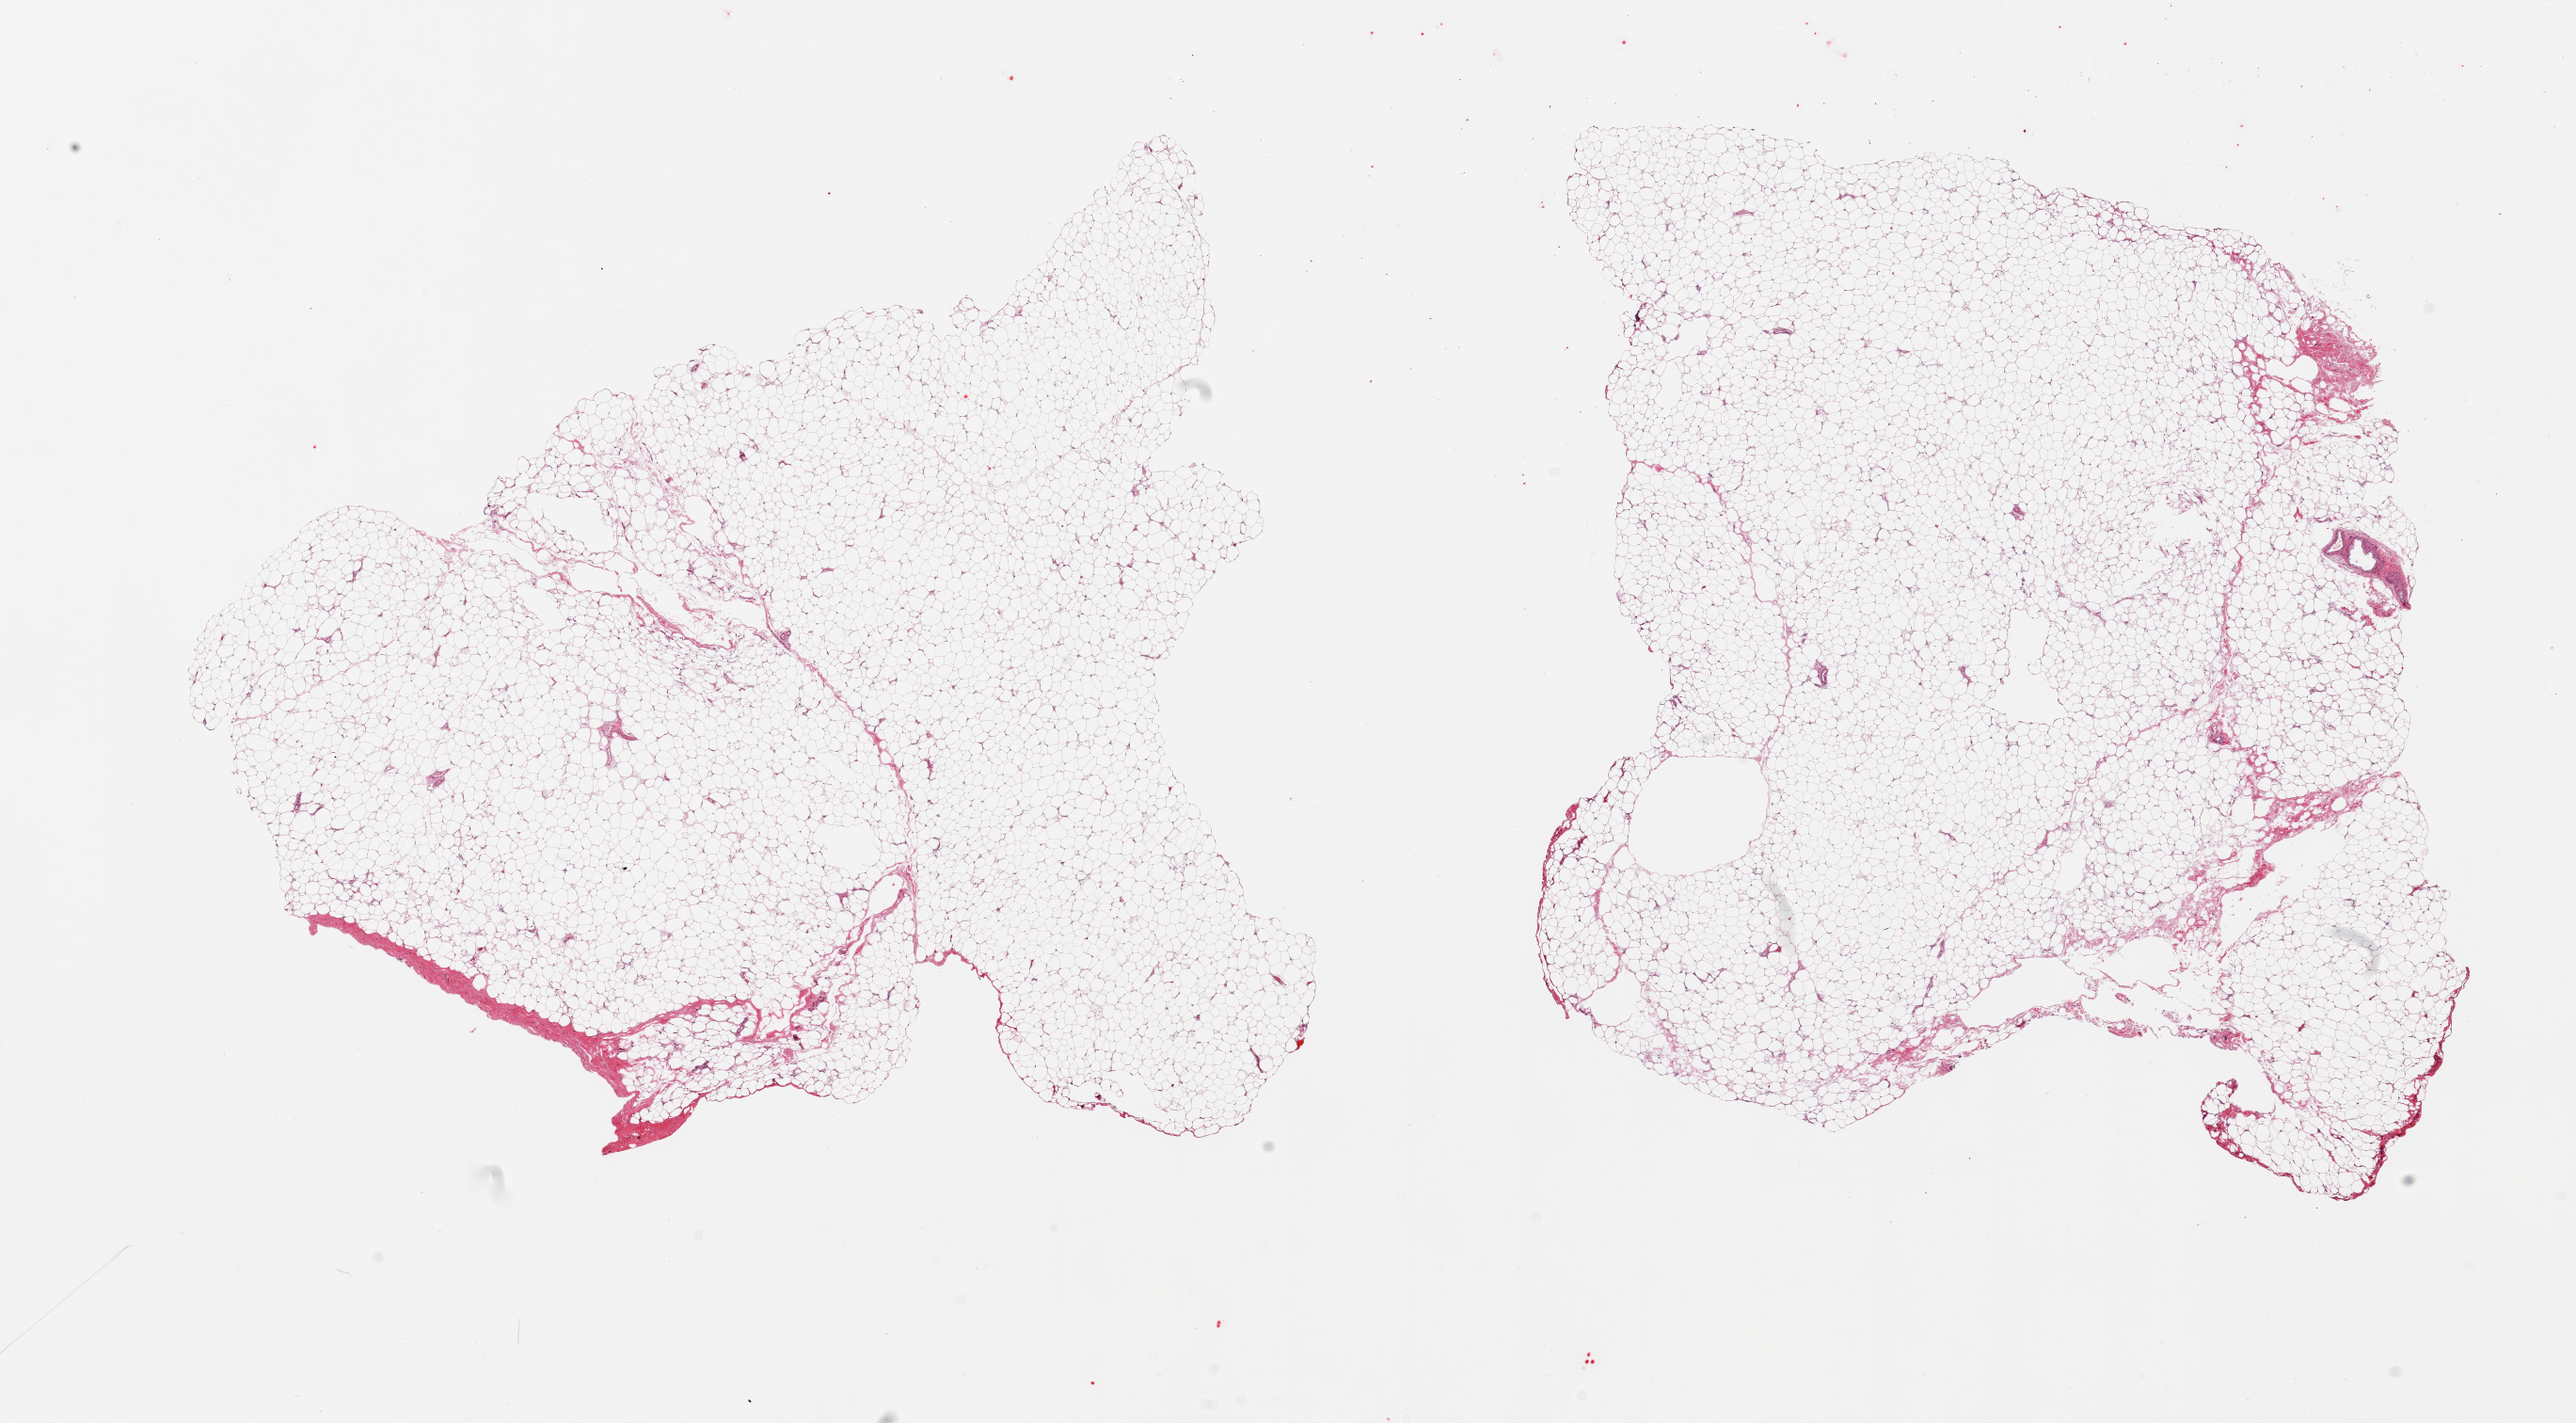
Haematoxylin and eosin whole-slide image — a low-resolution overview of the entire scanned area, about 21.7 x 12.0 mm (acquisition: 20x scan), PAXgene-fixed paraffin-embedded (PFPE) section, sampled site (target tissue): omentum, donor tissue sample. Donor sex: female.
Reviewer comment on this tissue sample: 2 pieces; mature adipose tissue.